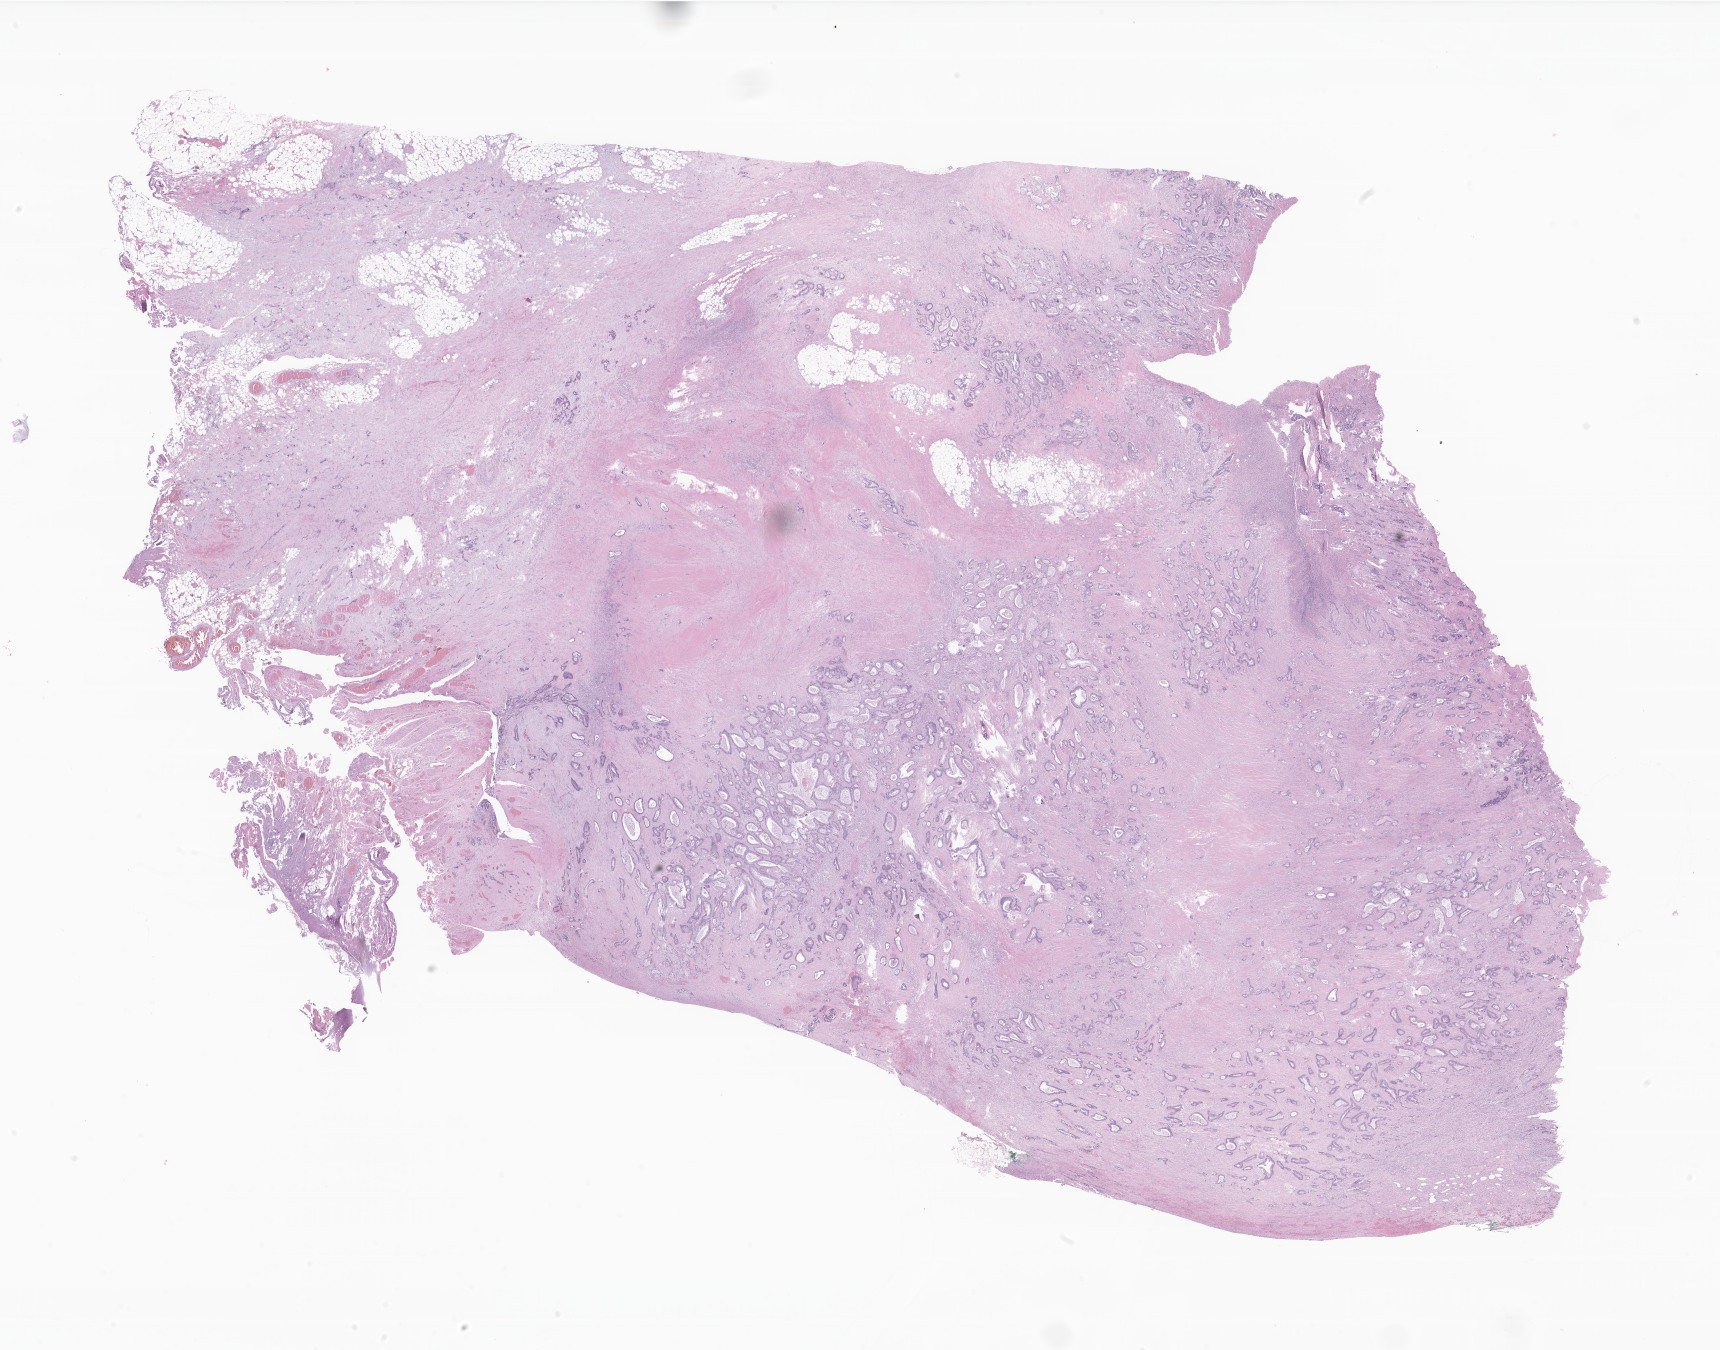
Digitized H&E-stained section of tumor tissue from the sigmoid colon — a low-resolution overview of the entire scanned area, about 29.0 x 22.8 mm, FFPE section. Patient: female, age 207 months (17 years 3 months).
Diagnosis (ICD-O-3 morphology term): Adenocarcinoma, NOS.